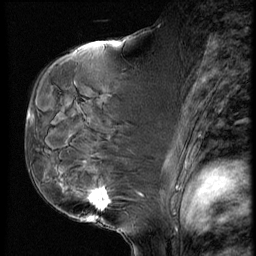
Breast MRI (dynamic contrast-enhanced), one sagittal slice. Slice 35 of 60 in the series (ordered by position). Dynamic contrast-enhanced series, image 2 of 4 at this slice position (ordered by acquisition). 1.5 T. TE 4.2 ms, TR 9 ms. 2.5 mm slice thickness. 256 × 256 image matrix. Female patient, age 50 years. Case-level facts recorded for this patient, not image findings: setting: breast cancer imaged before/during neoadjuvant chemotherapy; receptor status: HR-positive, HER2-negative.
Structures marked on this image (semi-automatically segmented with operator editing):
- analysis volume of interest (the breast-tissue region the enhancement analysis was run in; not a lesion): bounding box <48,109,135,230> (left, top, right, bottom; pixels)
- tumour enhancement mask (voxels above the 140 % enhancement threshold inside the analysis volume of interest): <88,190,109,207>